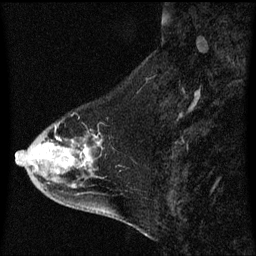
Breast MRI (dynamic contrast-enhanced), one sagittal slice; position 21 of 60 along the scan axis; dynamic contrast-enhanced series, image 2 of 3 at this slice position (ordered by acquisition); 1.5 T; TE 4.2 ms, TR 8.4 ms; 256 × 256 image matrix. Patient: female, 46 years. Case-level facts recorded for this patient, not image findings: setting: breast cancer imaged before/during neoadjuvant chemotherapy; receptor status: HER2-positive.
Outlined on this slice (semi-automatic segmentation, software-assisted and operator-edited):
- analysis volume of interest (the breast-tissue region the enhancement analysis was run in; not a lesion): bounding box (x1, y1, x2, y2) in pixels: (18, 124, 104, 195)
- tumour enhancement mask (voxels above the 70 % enhancement threshold inside the analysis volume of interest): (57, 138, 89, 165)